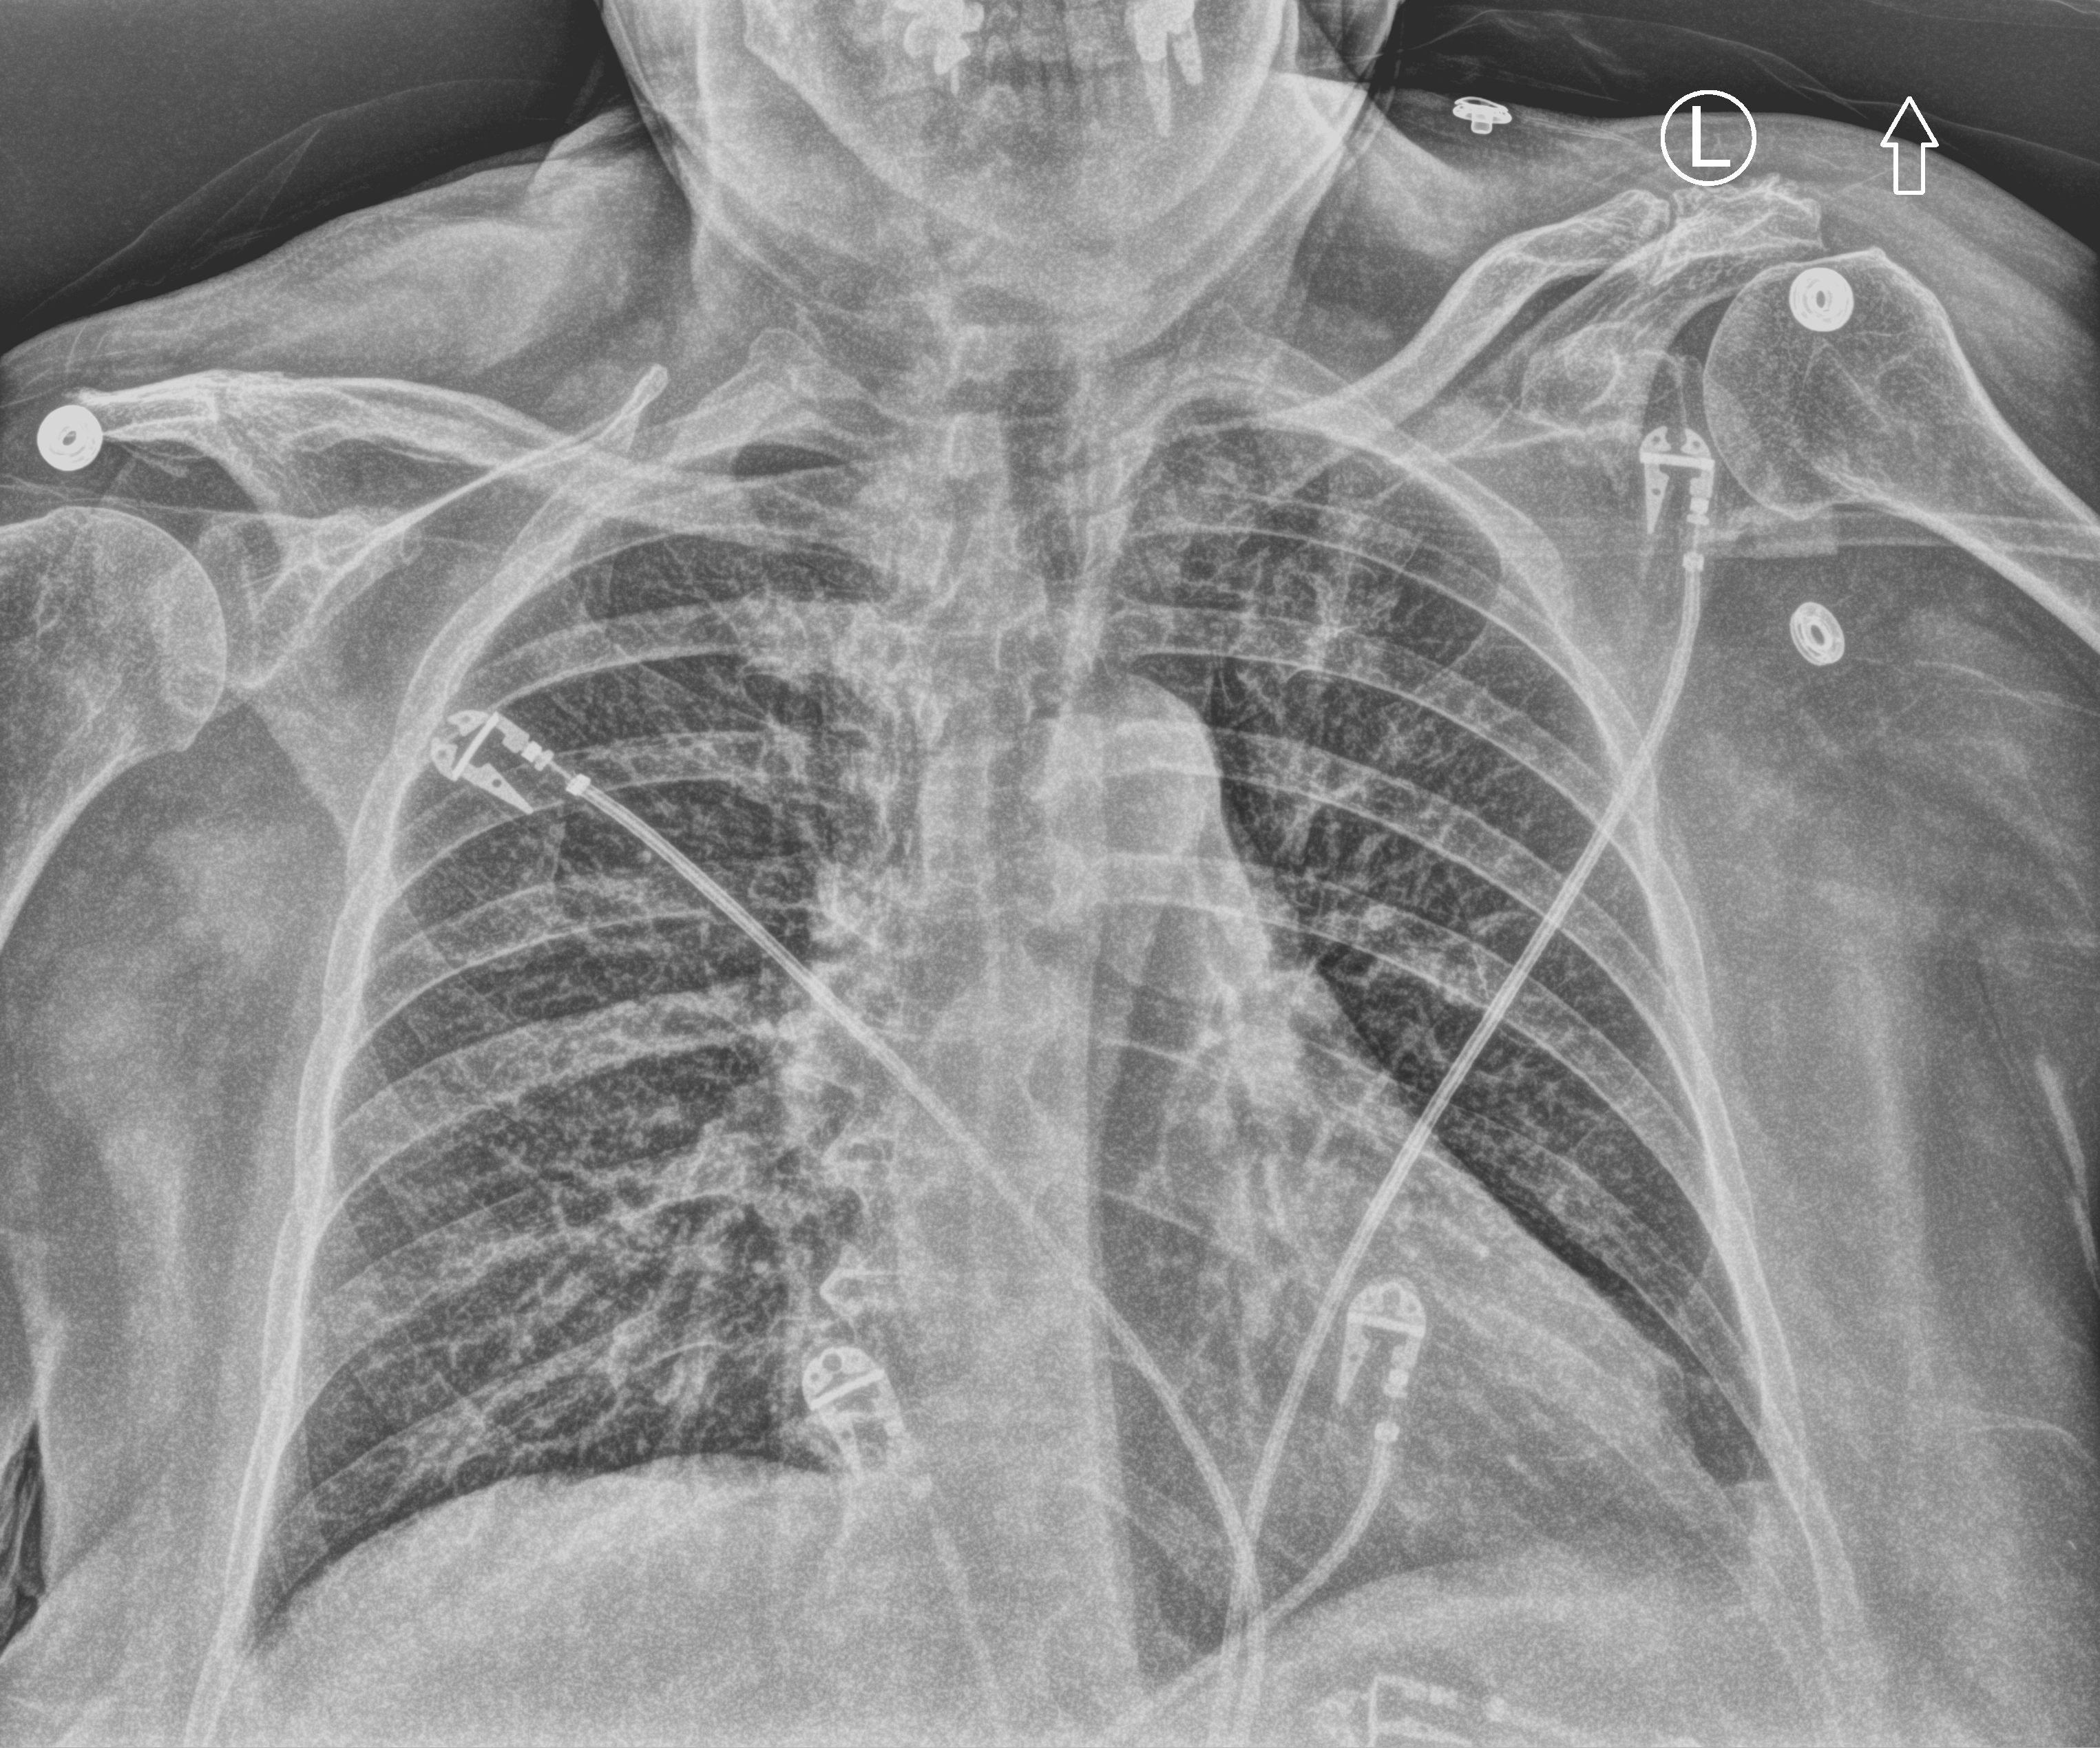
Portable chest radiograph, anteroposterior (AP) projection. Female patient hospitalised with COVID-19, age 60–74 years.
Hospital-stay facts (about this admission, not read from this image; timing relative to this image not recorded): COPD (admission record): no; chronic kidney disease (admission record): no; admitted to intensive care during this hospital stay: no.